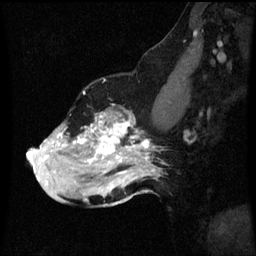
Breast MRI (dynamic contrast-enhanced), one sagittal slice; position 38 of 60 along the scan axis; dynamic contrast-enhanced series, image 2 of 3 at this slice position (ordered by acquisition); 1.5 T; TE 4.2 ms, TR 8.9 ms; 256 × 256 image matrix, field of view 200 × 200 mm. Female patient, age 49 years. From the clinical record (not read from this slice): setting: breast cancer imaged before/during neoadjuvant chemotherapy; receptor status: HR-positive, HER2-negative.
Structures marked on this image (semi-automatic segmentation, software-assisted and operator-edited):
- analysis volume of interest (the breast-tissue region the enhancement analysis was run in; not a lesion): bounding box <28,108,159,199> (left, top, right, bottom; pixels)
- tumour enhancement mask (voxels above the 70 % enhancement threshold inside the analysis volume of interest): <28,114,155,185>